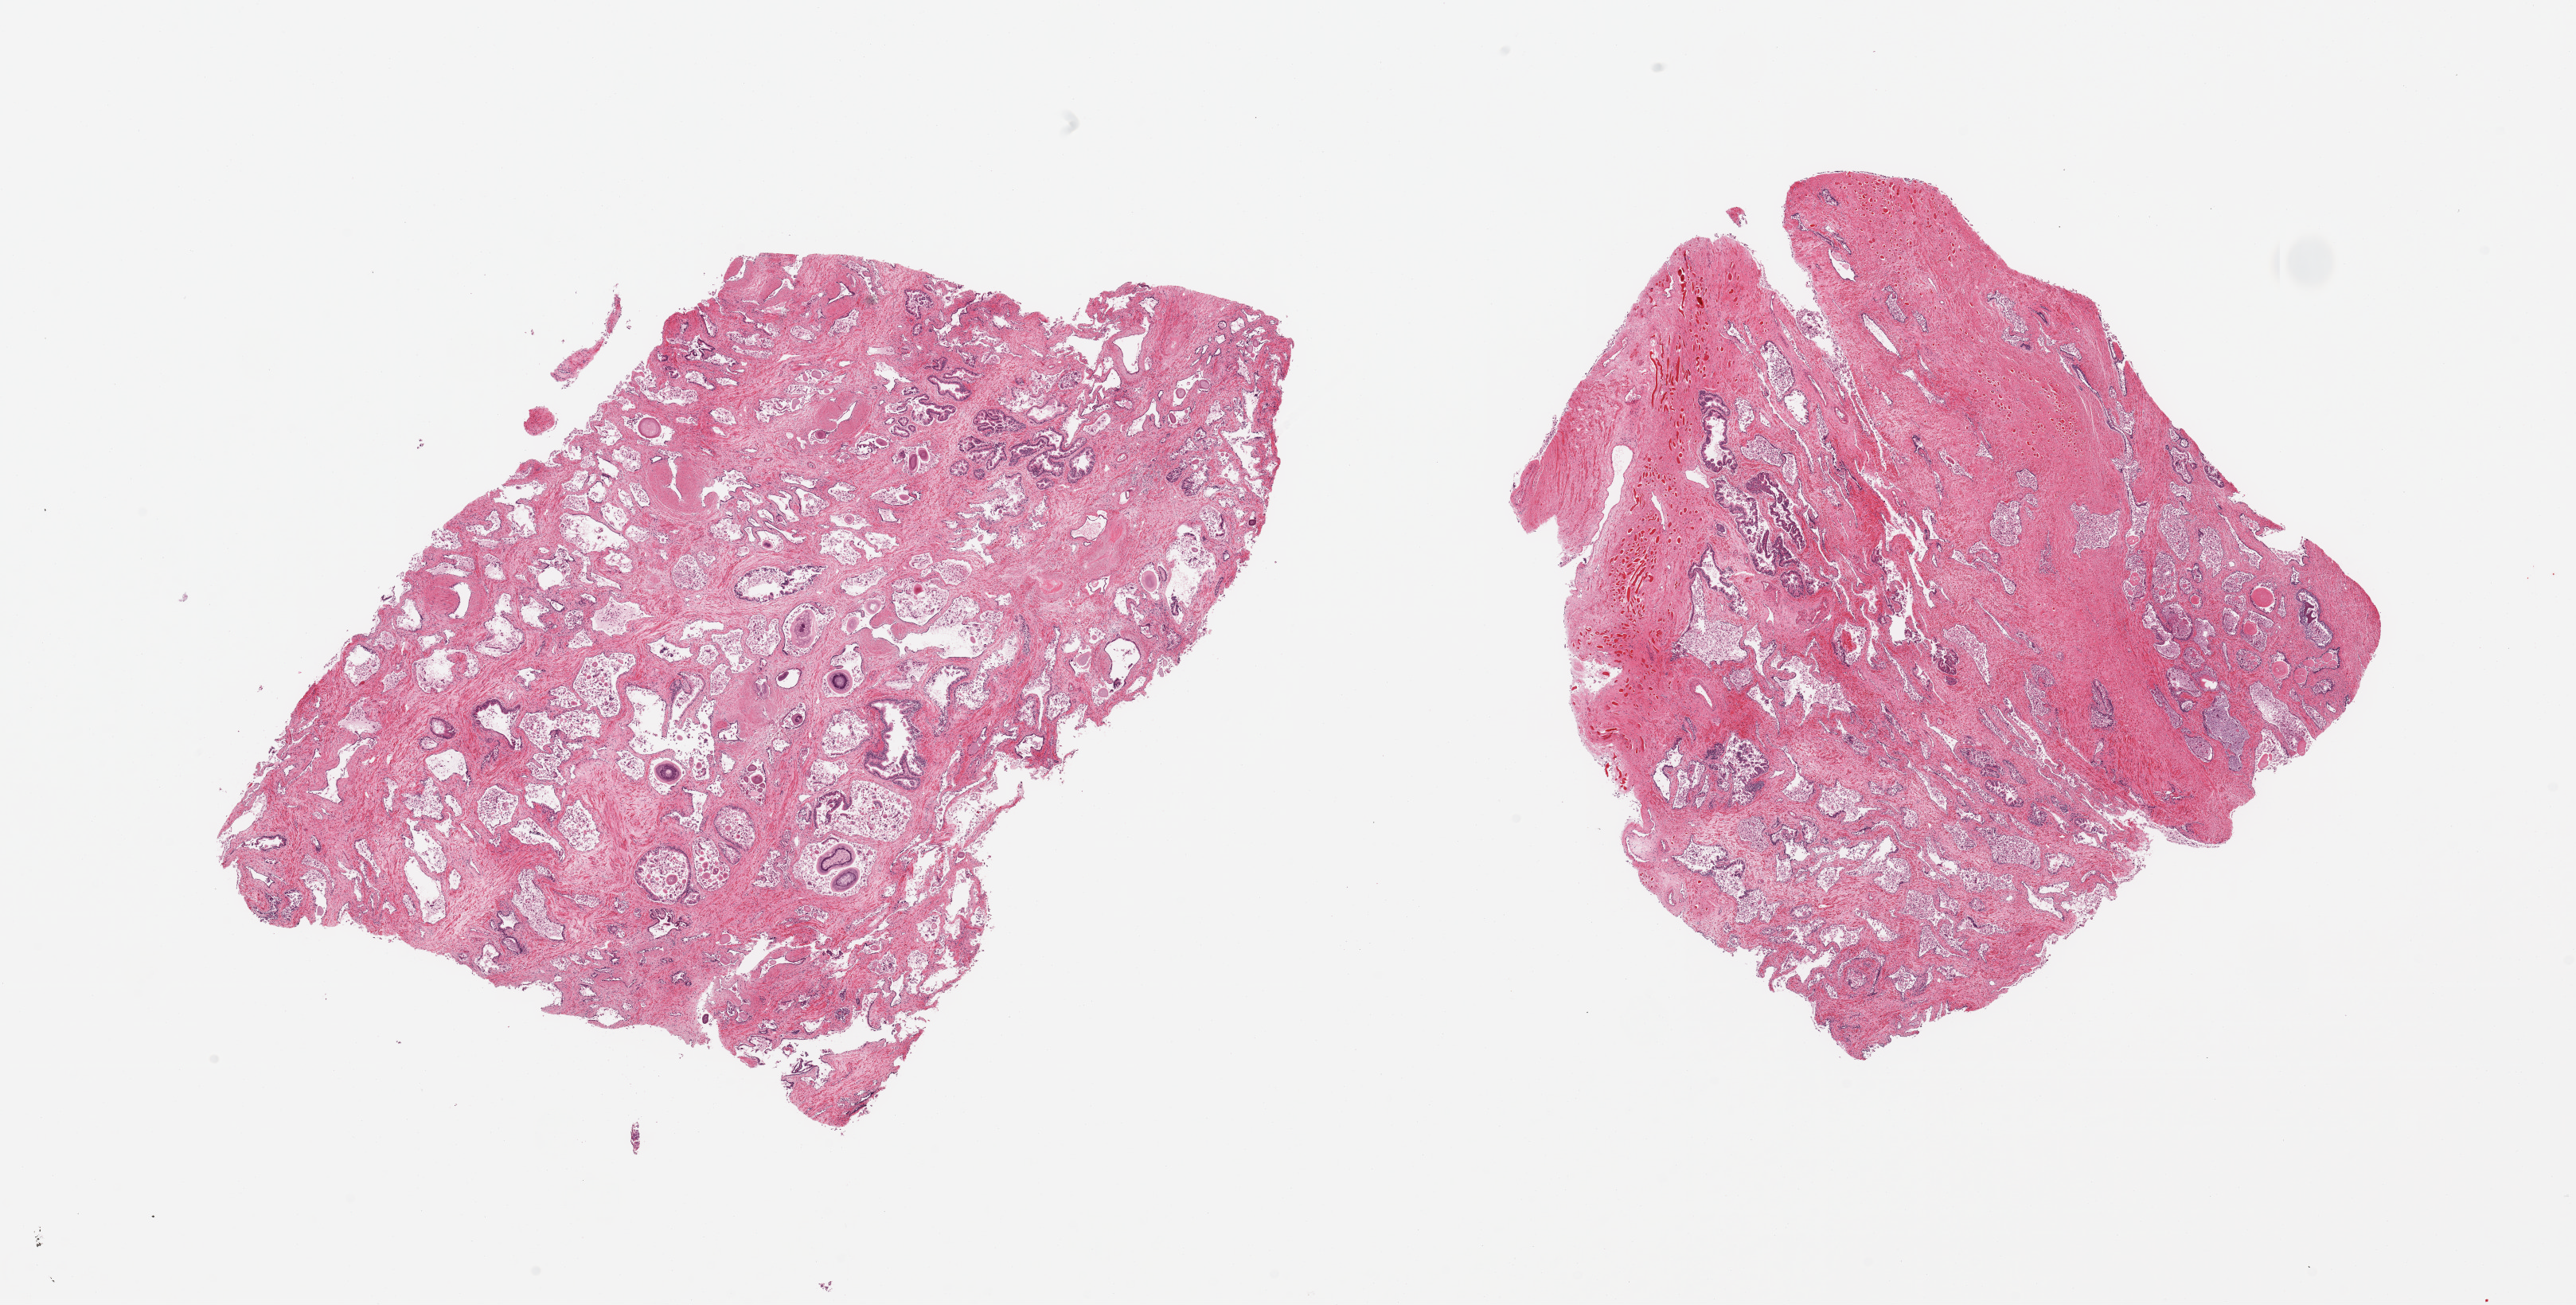
Whole-slide image, hematoxylin and eosin (H&E) stain — shown as a low-resolution overview of the whole scanned area (about 25.6 x 13.0 mm, slide scanned at 20x). PAXgene-fixed, paraffin-embedded tissue. Section of prostate (target tissue). Donor tissue sample. Donor sex: male.
Review note (as recorded): 2 pieces, hyperplastic glandular pattern, glandular elements with advanced autolysis.